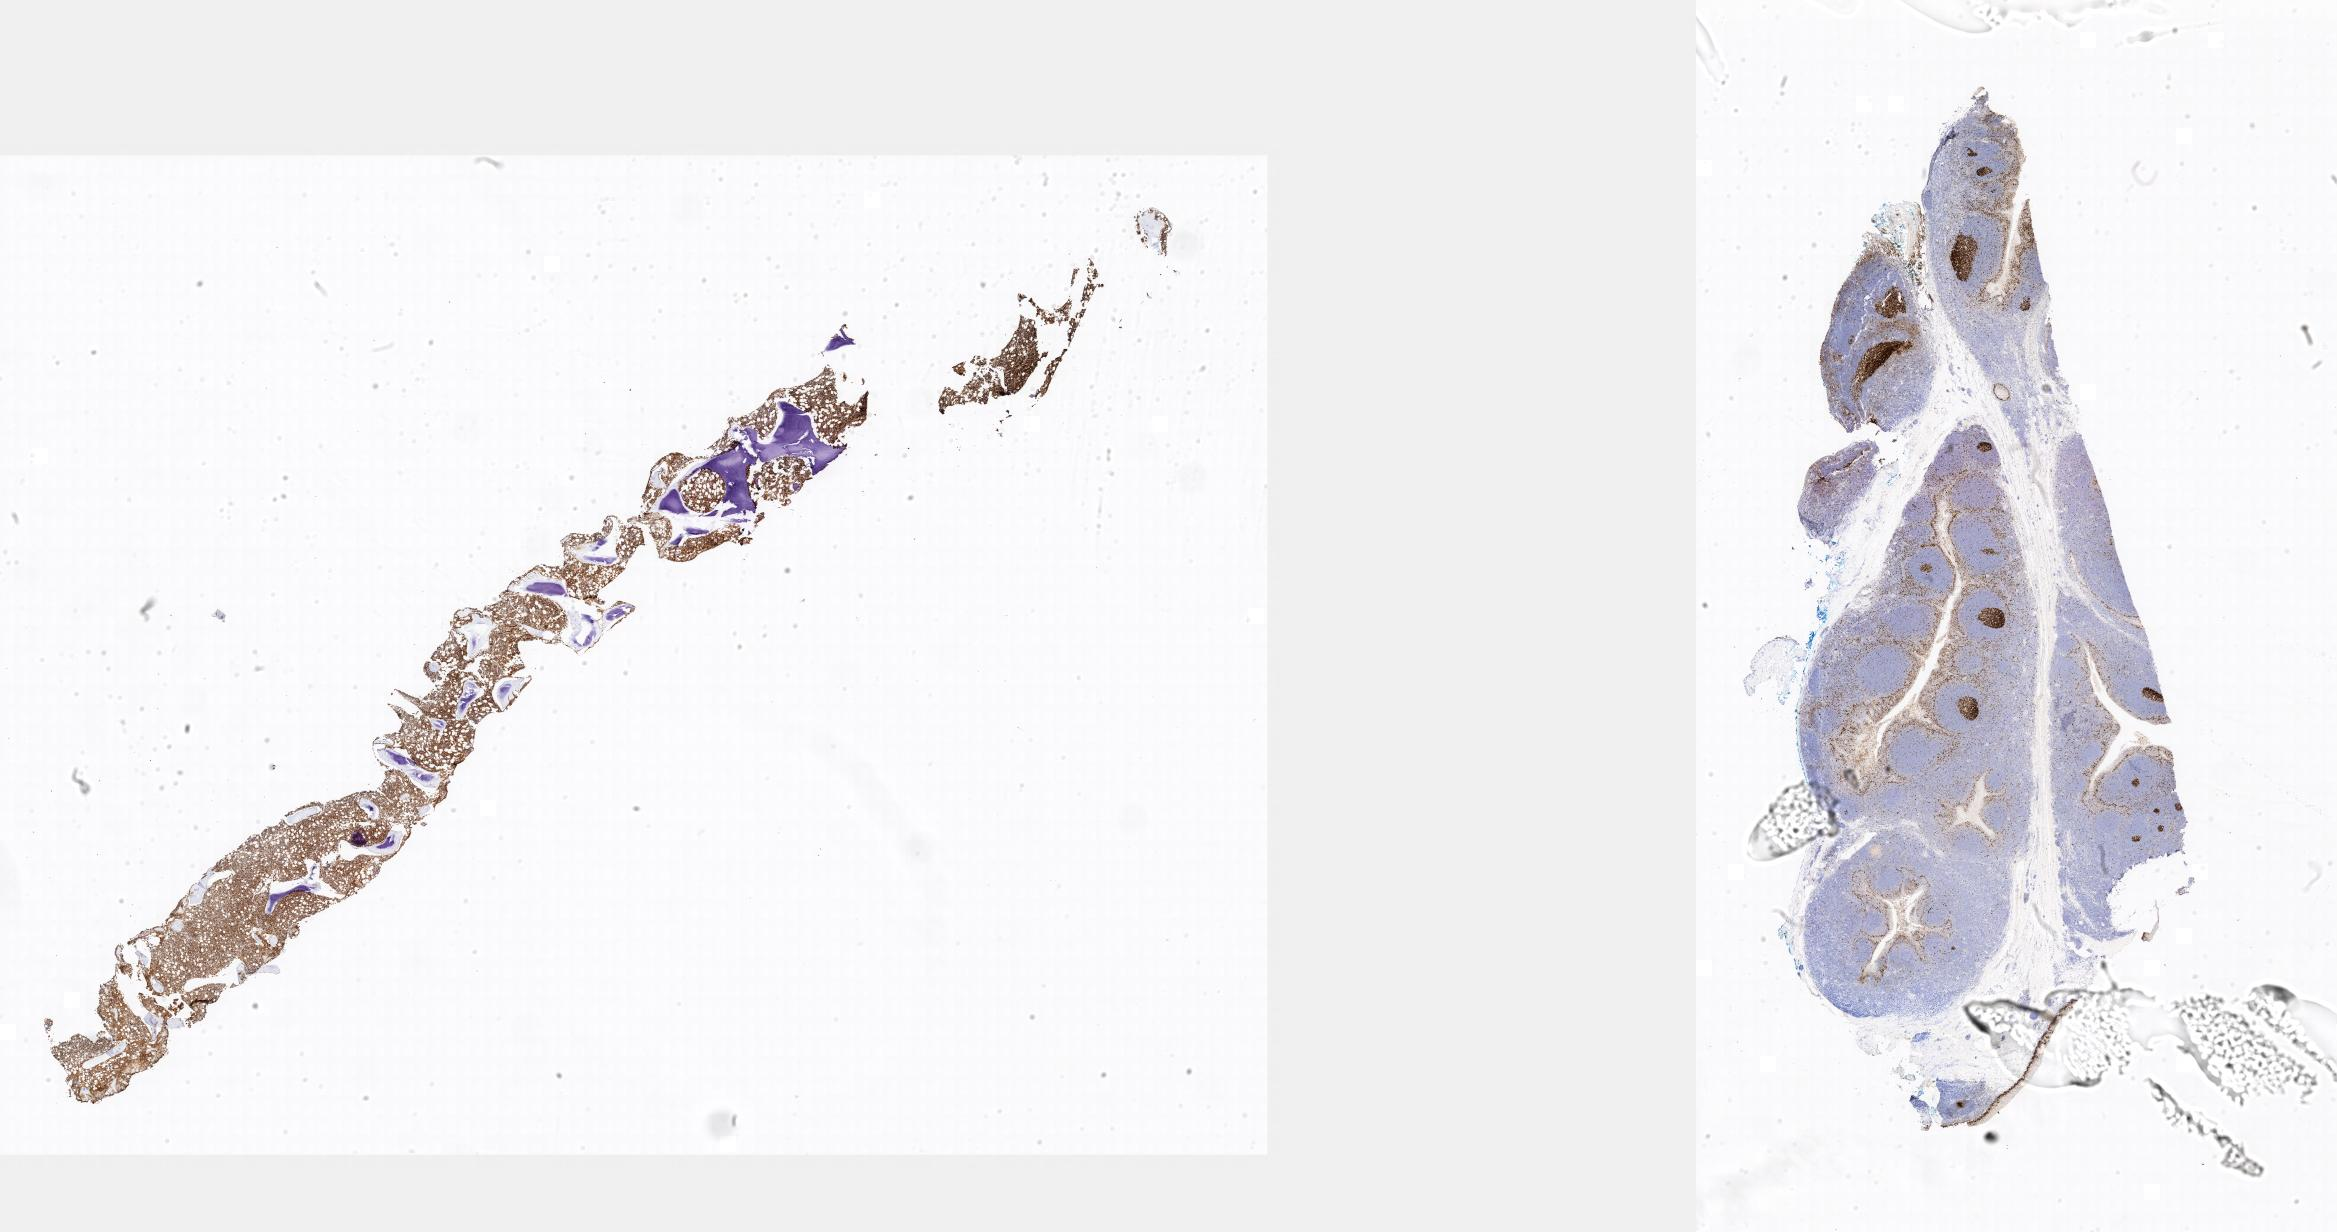
IHC for Ki-67, whole-slide image — low-resolution overview of the scanned area. Specimen: tumor tissue. Anatomic site: bone marrow. Patient: male, aged 20.
* diagnosis: Diffuse large B-cell lymphoma, NOS